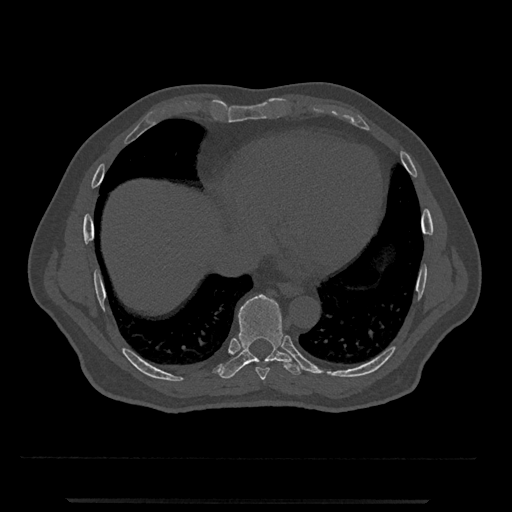
CT including the spine, one axial slice. Reconstruction kernel Br40s/3. 120 kVp. Bone window (W 1800 / L 400 HU). 0.5 mm slice thickness. 512 × 512 image matrix, field of view 419 × 419 mm. Male patient, age 63 years. From the clinical record (not read from this slice): primary cancer: prostate.
Structures marked on this image (semi-automatically segmented with operator editing):
- T8 vertebra: bounding box <256,367,270,380> (left, top, right, bottom; pixels)
- T9 vertebra: <219,294,303,379>